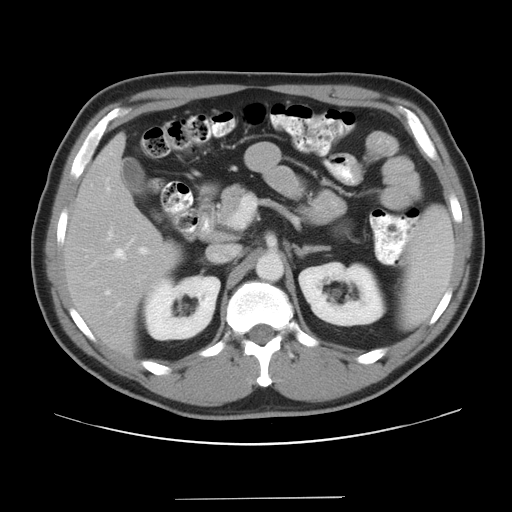
Contrast-enhanced abdominal CT, one axial slice; slice 21 of 37 in the series (ordered by position); reconstruction kernel STANDARD; intravenous contrast given; soft-tissue window (W 400 / L 40 HU); 7.5 mm slice thickness; 512 × 512 image matrix, field of view 400 × 400 mm. Male patient, age 46 years. Case-level facts recorded for this patient, not image findings: diagnosis: colorectal cancer liver metastases, imaged before liver resection; multiple liver metastases: yes; largest metastasis: 1 cm.
Outlined on this slice (outlined manually by an expert reader):
- hepatic veins: bounding box <105,232,126,295> (left, top, right, bottom; pixels)
- liver: <66,138,176,352>
- planned liver remnant (the part of the liver to remain after resection): <66,138,176,352>
- portal vein (with intrahepatic branches): <140,247,147,254>